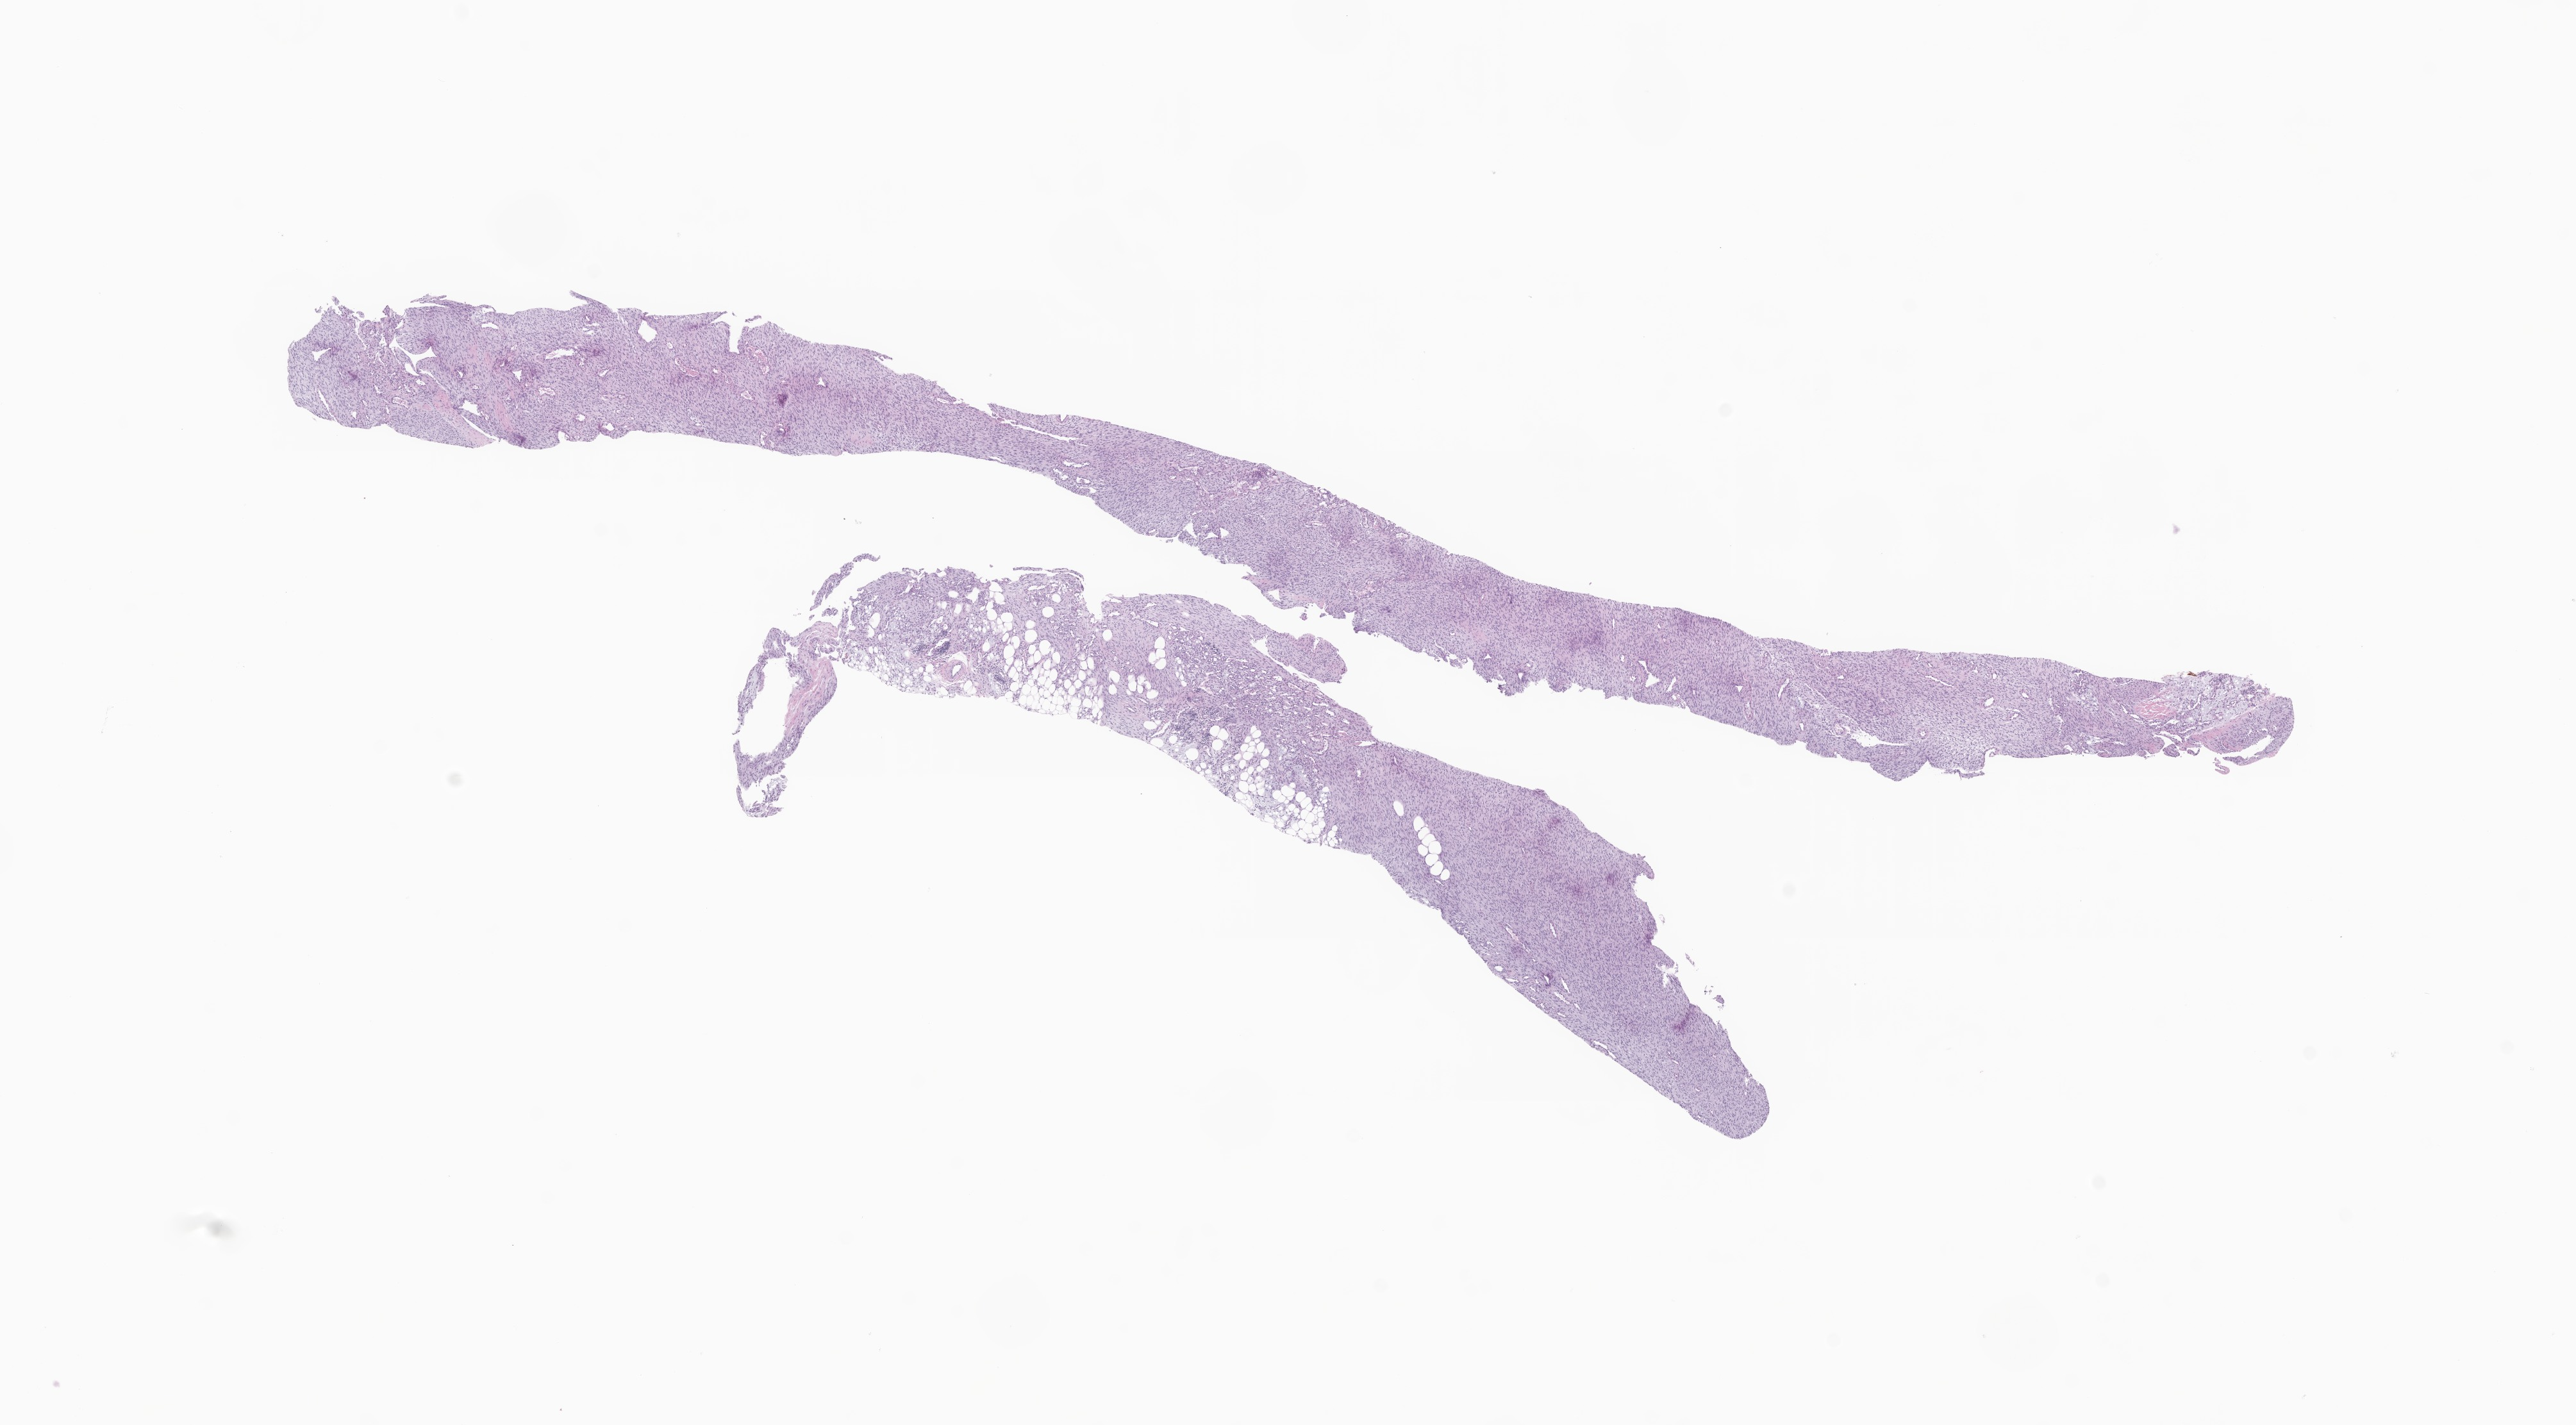
Whole-slide image, H&E stain of tumor tissue from the soft tissue of lower extremity, low-resolution overview of the scanned area, about 16.9 x 9.4 mm; FFPE section. Female patient, age 34 days.
• diagnosis (ICD-O-3 morphology term): Malignant tumor, spindle cell type